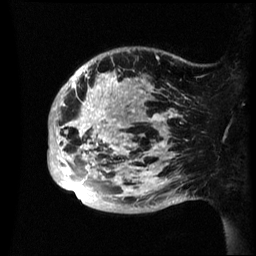
Breast MRI (dynamic contrast-enhanced), one sagittal slice. Slice 14 of 60 in the series (ordered by position). Dynamic contrast-enhanced series, image 2 of 3 at this slice position (ordered by acquisition). 1.5 T. TE 4.2 ms, TR 8.4 ms. 2.4 mm slice thickness. 256 × 256 image matrix, field of view 230 × 230 mm. Female patient, age 48 years.
Annotated regions visible in this slice (semi-automatic segmentation, software-assisted and operator-edited):
- analysis volume of interest (the breast-tissue region the enhancement analysis was run in; not a lesion): bounding box [x1, y1, x2, y2] px = [48, 48, 193, 214]
- tumour enhancement mask (voxels above the 70 % enhancement threshold inside the analysis volume of interest): [48, 70, 178, 198]